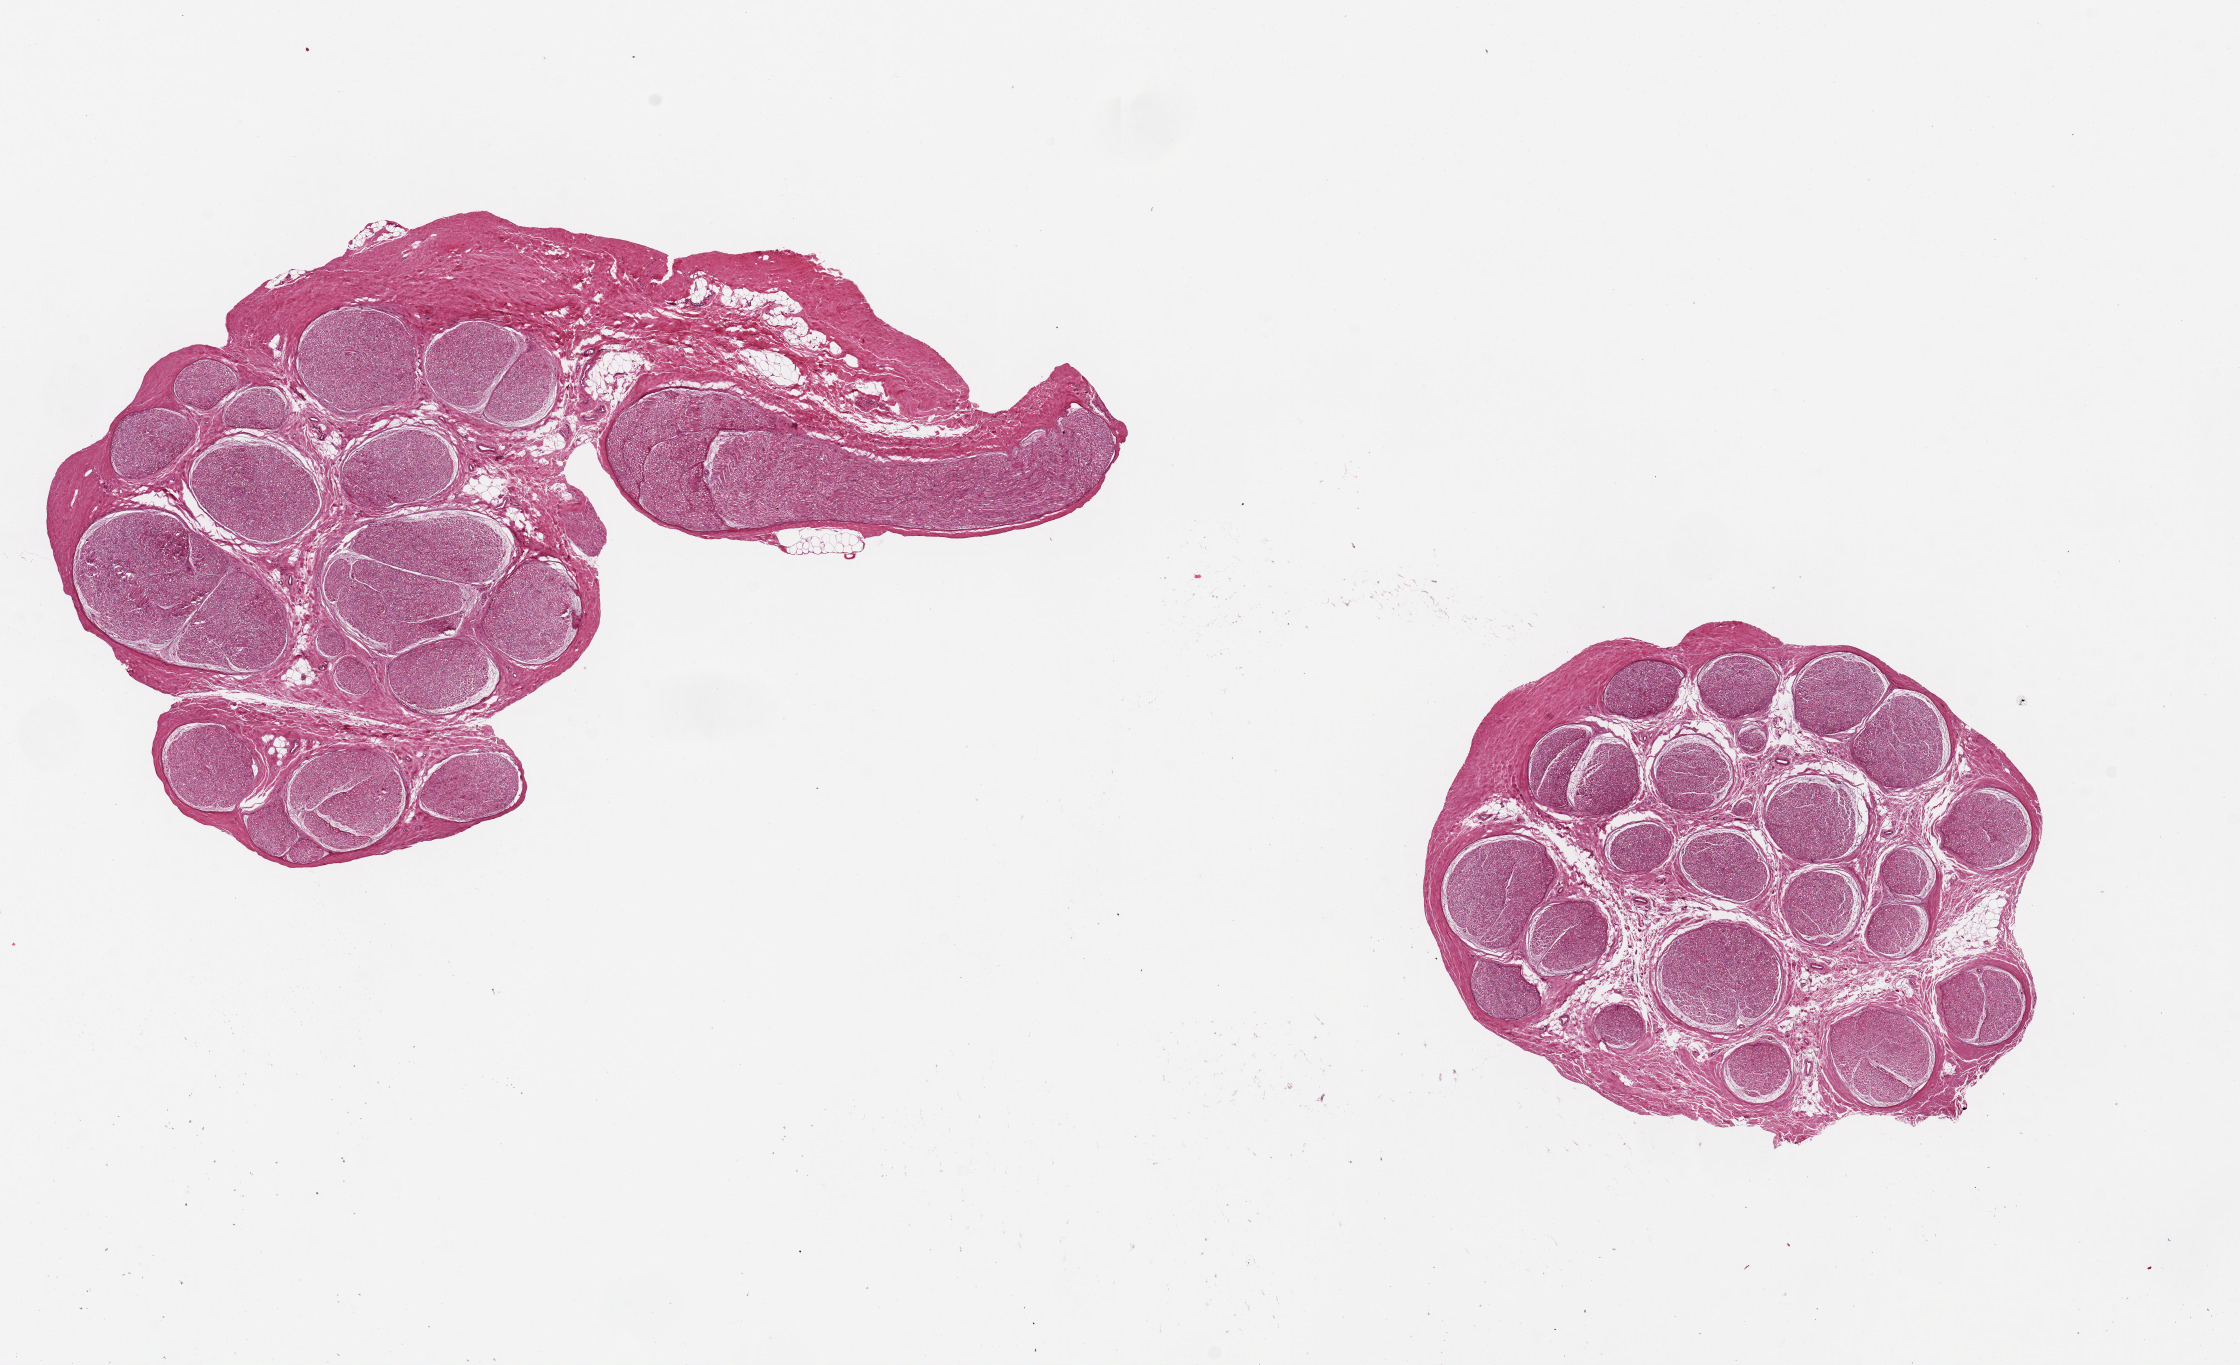
Haematoxylin and eosin whole-slide image — low-resolution overview of the scanned area, about 17.7 x 10.8 mm. PAXgene-fixed, paraffin-embedded tissue. Target tissue: tibial nerve. Tissue donor sample. Male donor.
* pathologist's review note for this sample: 2 pieces, ~4.5-5mm d. Excellent clean specimens, minimal fat